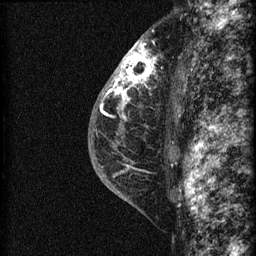
Breast MRI (dynamic contrast-enhanced), one sagittal slice. Slice 42 of 60 in the series (ordered by position). Dynamic contrast-enhanced series, image 2 of 3 at this slice position (ordered by acquisition). 1.5 T. TE 4.2 ms, TR 22.7 ms. 256 × 256 image matrix, field of view 180 × 180 mm. Patient: female, 48 years. Case-level facts recorded for this patient, not image findings: setting: breast cancer imaged before/during neoadjuvant chemotherapy; receptor status: triple-negative.
Structures marked on this image (semi-automatically segmented with operator editing):
- analysis volume of interest (the breast-tissue region the enhancement analysis was run in; not a lesion): bounding box (x1, y1, x2, y2) in pixels: (115, 34, 169, 162)
- tumour enhancement mask (voxels above the 90 % enhancement threshold inside the analysis volume of interest): (115, 41, 156, 109)